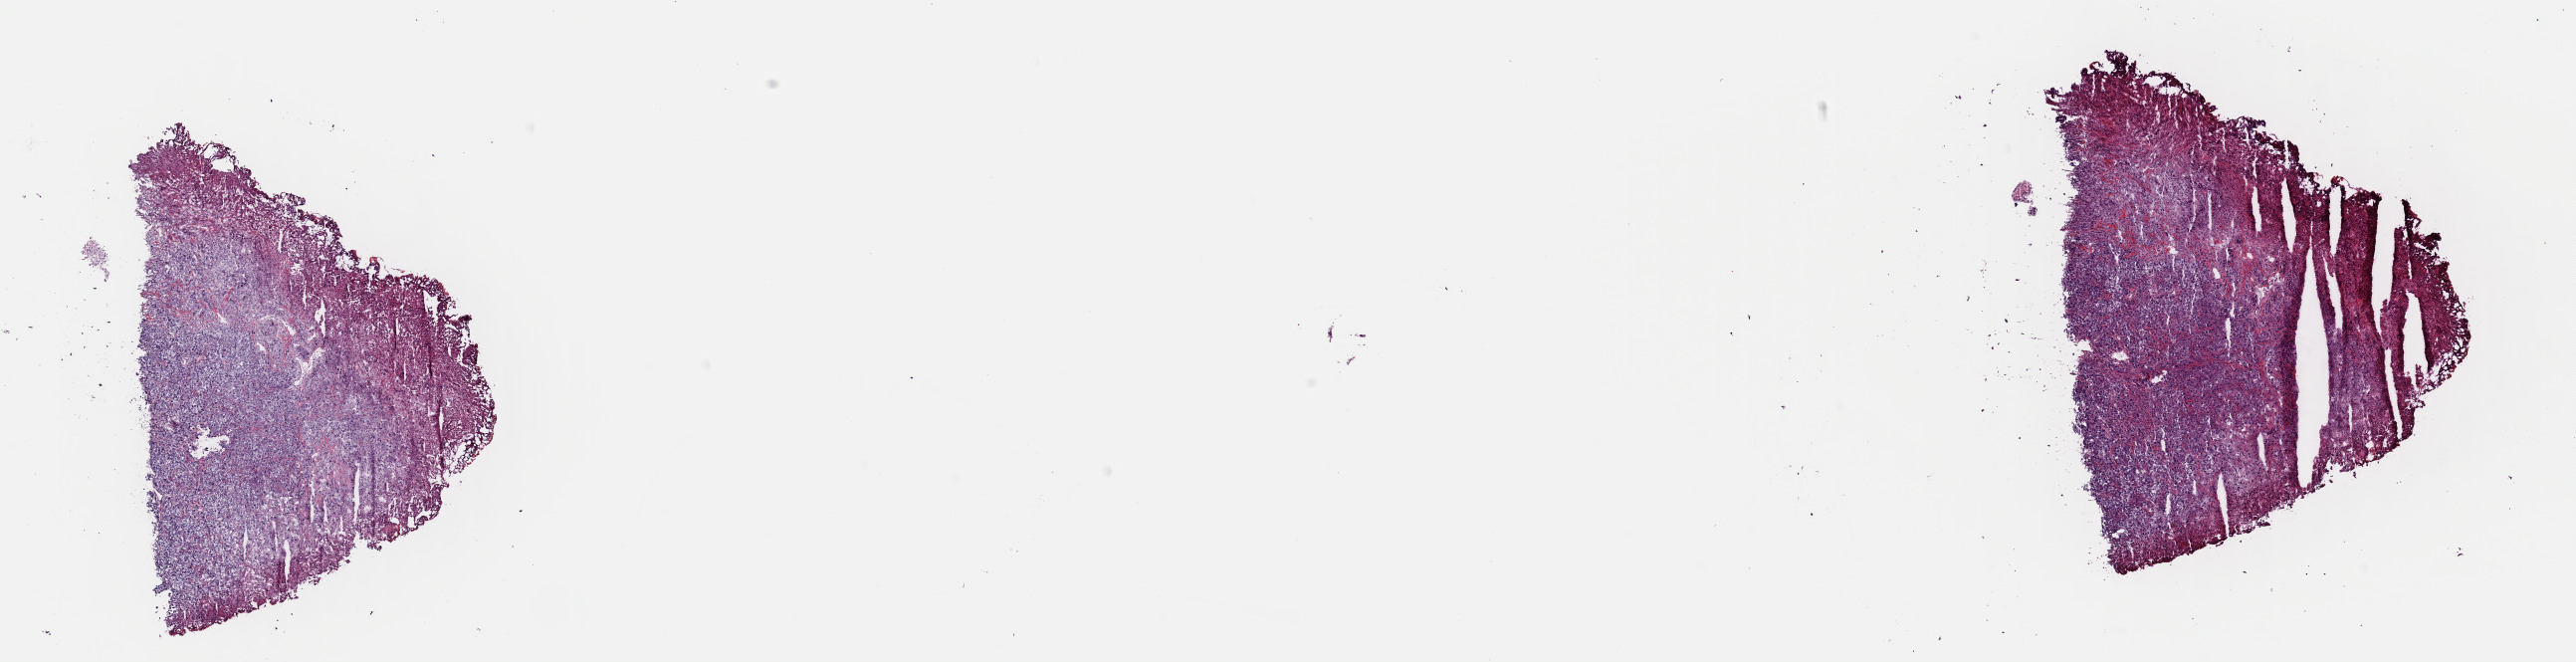
Whole-slide histology image, H&E, low-resolution overview of the scanned area, about 20.4 x 5.3 mm, frozen section, primary tumour sample from the bladder. Male patient; age at initial diagnosis 75 years. Histologic grade: high grade. Composition of this section per pathologist review: tumour cells 95%, tumour nuclei 85%, normal cells 0%, stromal cells 0%, necrosis 5%. Inflammatory infiltration, as recorded: lymphocyte infiltration 2%, monocyte infiltration 1%, neutrophil infiltration 0%.
Diagnosis: Transitional cell carcinoma. TNM: NX MX. AJCC pathologic stage: II.